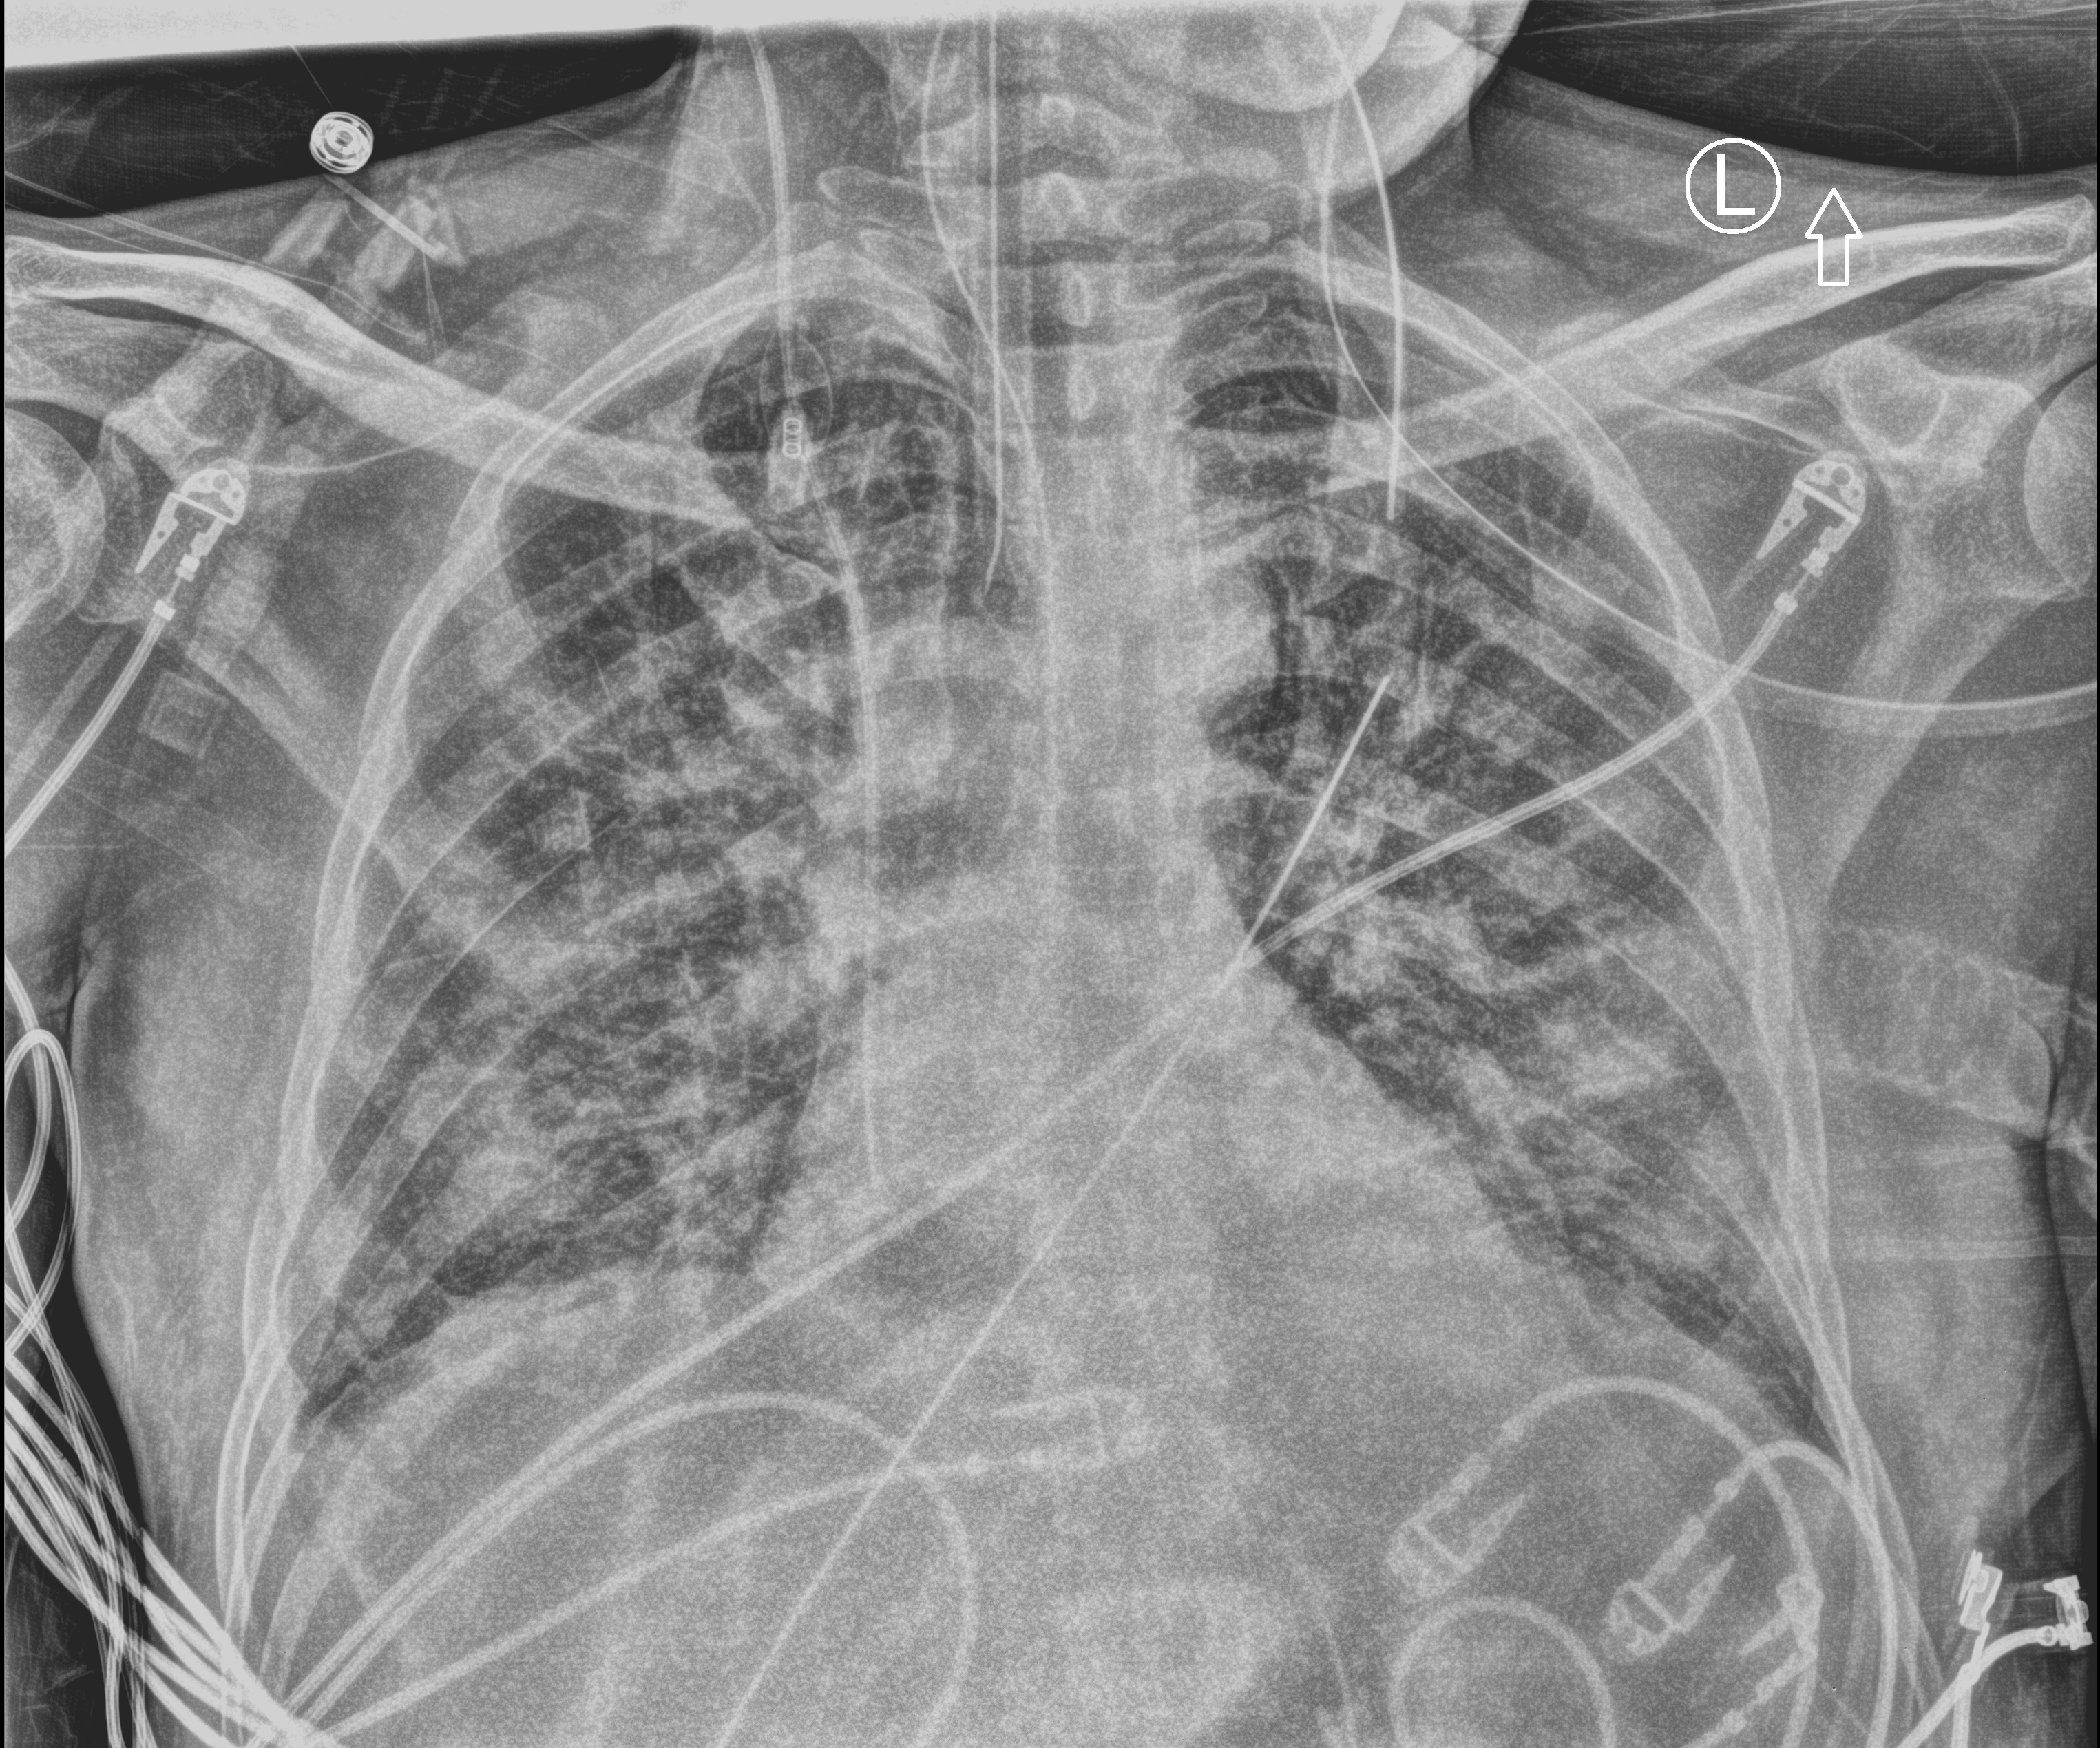
Bedside chest radiograph (computed radiography), anteroposterior (AP) projection. Patient hospitalised with COVID-19; male, aged 18–59 years.
Hospital-stay facts (about this admission, not read from this image; timing relative to this image not recorded): length of hospital stay: 41 days; admitted to intensive care during this hospital stay: yes.